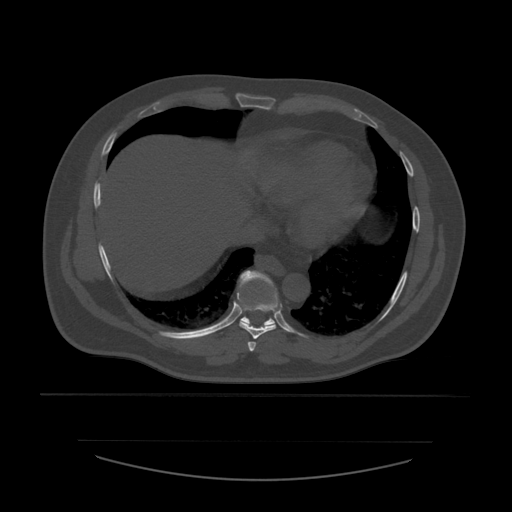
CT including the spine, one axial slice; slice 331 of 532 in the series (ordered by position); bone window (W 1800 / L 400 HU); 1.25 mm slice thickness; 512 × 512 image matrix, field of view 441 × 441 mm. Patient age 44 years. Case-level facts recorded for this patient, not image findings: primary cancer: soft tissue sarcoma.
Structures marked on this image (semi-automatic segmentation, software-assisted and operator-edited):
- T7 vertebra: bounding box <248,342,257,353> (left, top, right, bottom; pixels)
- T8 vertebra: <239,298,278,340>
- T9 vertebra: <237,271,278,326>